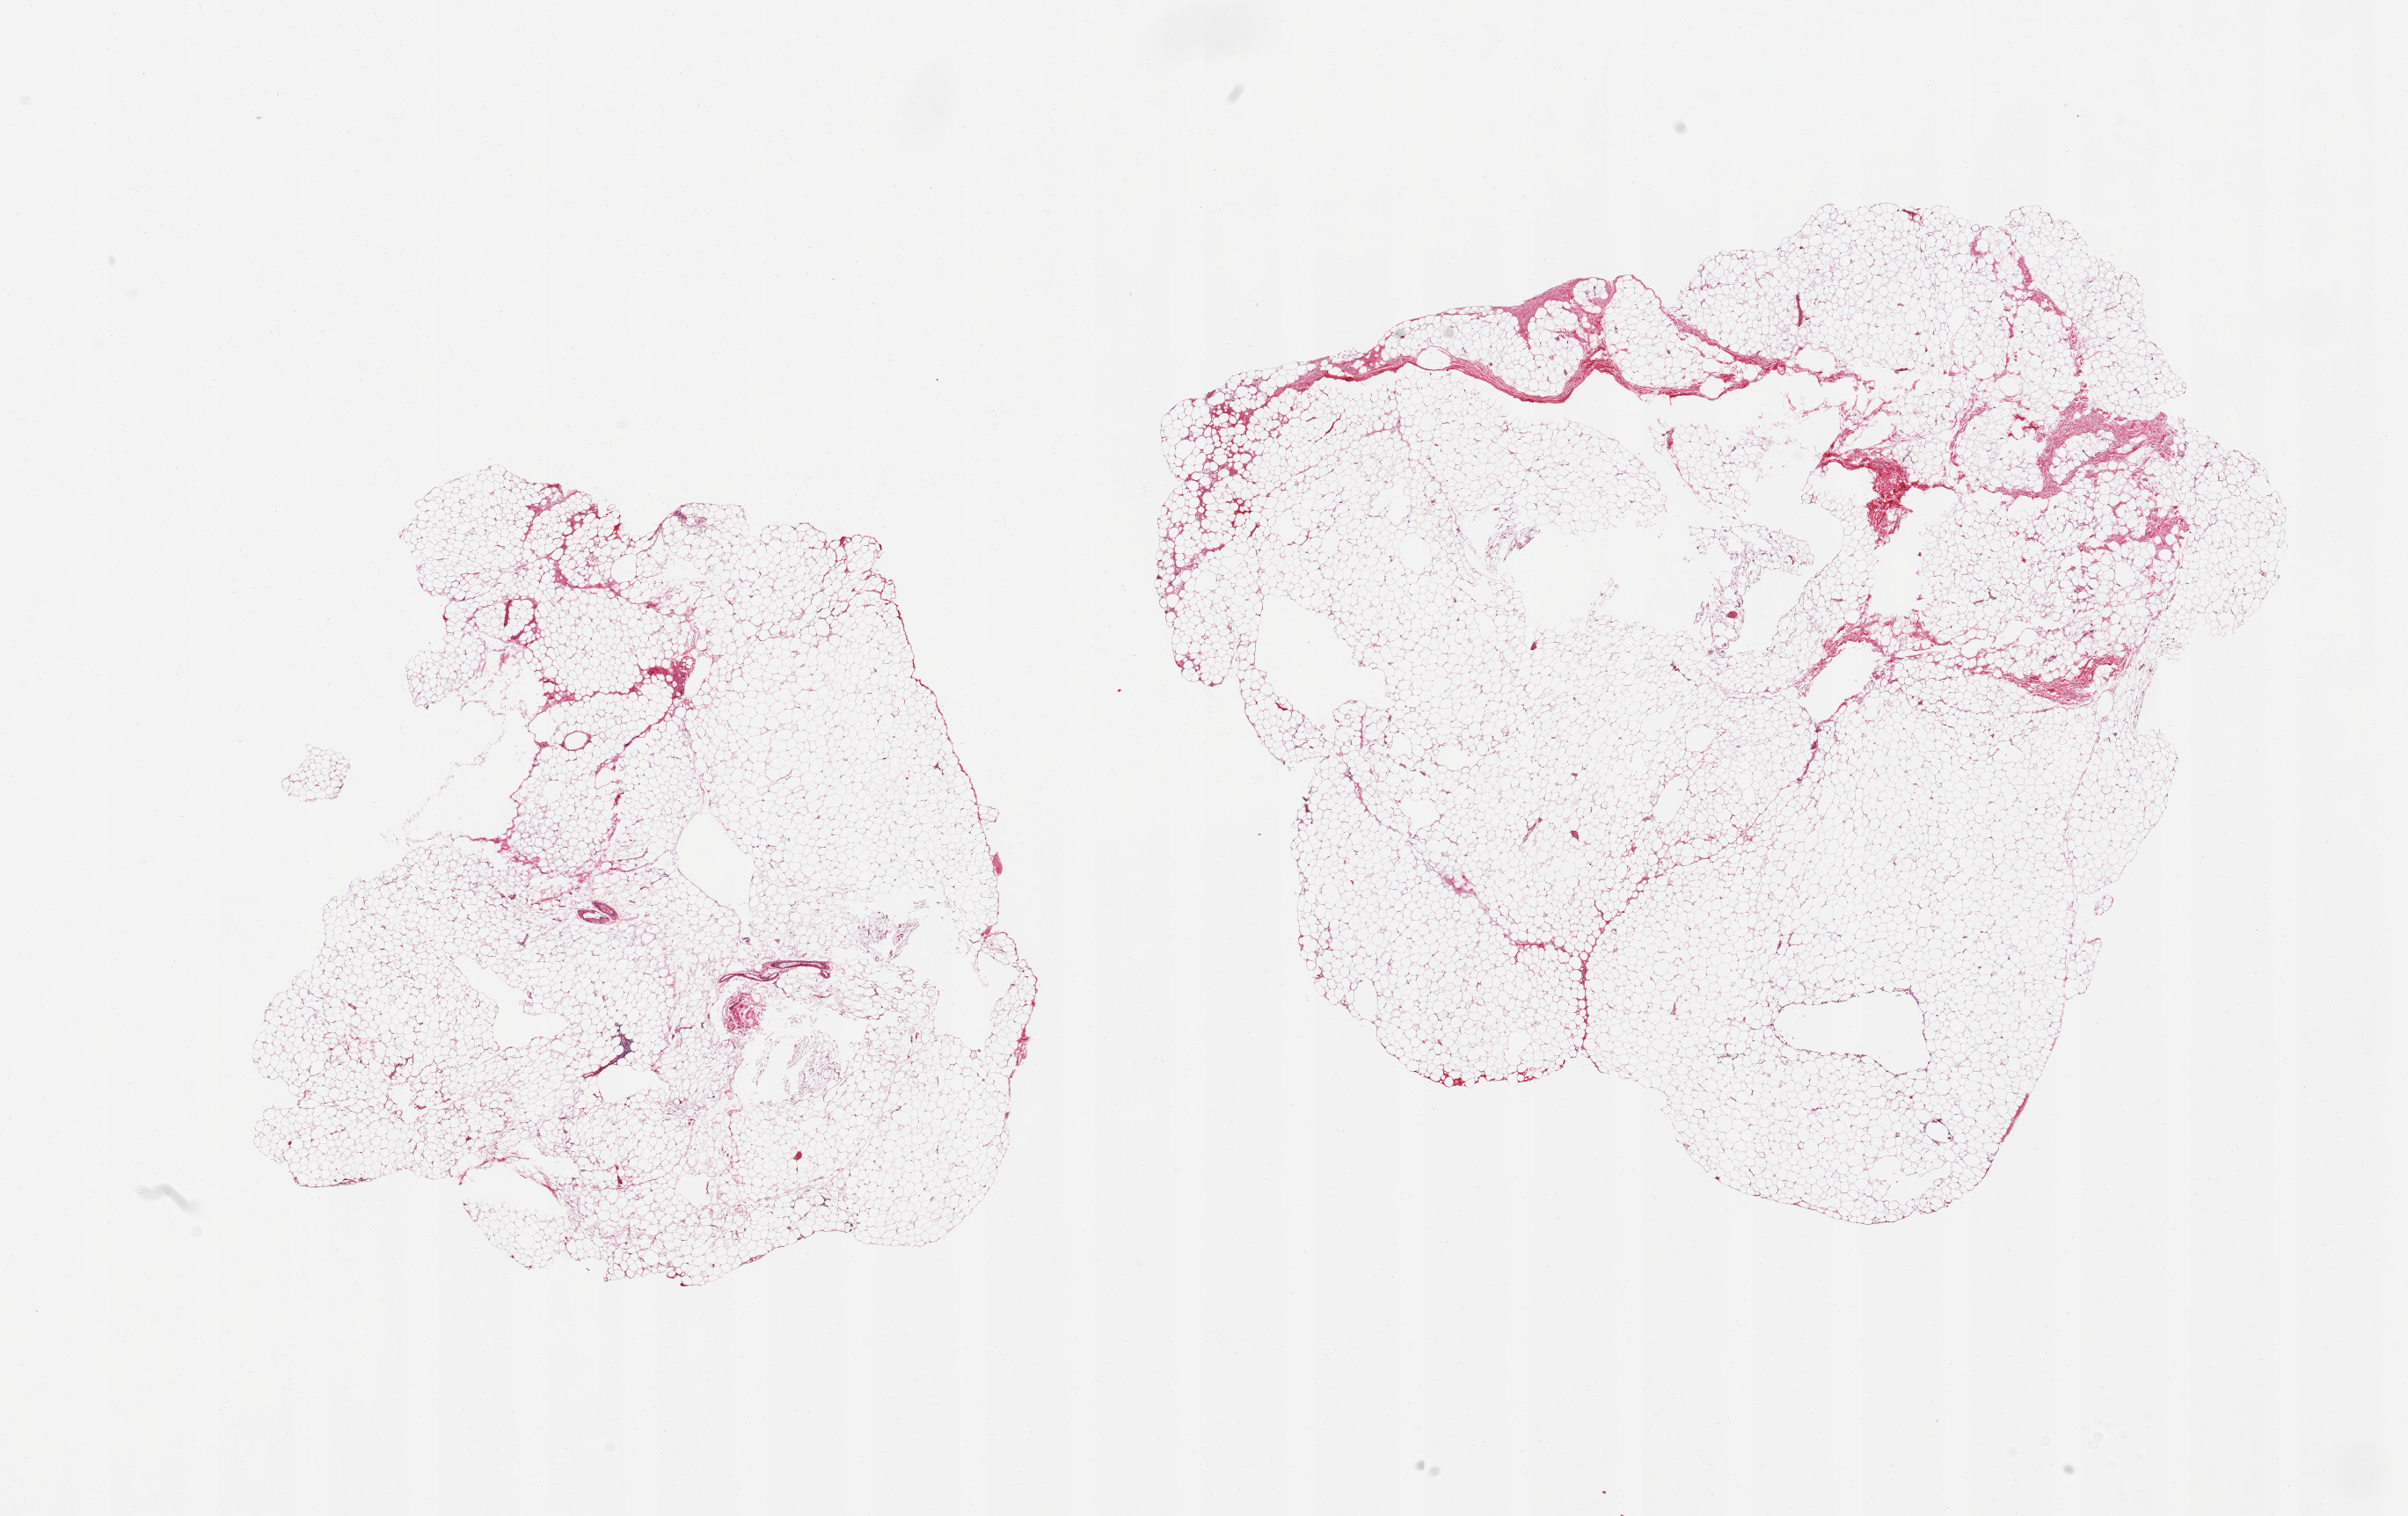
Digitized haematoxylin and eosin-stained section, a low-resolution overview of the entire scanned area, about 21.7 x 13.6 mm, PAXgene-fixed paraffin-embedded (PFPE) section, target tissue: breast, tissue donor sample. Donor sex: male.
Reviewer comment on this tissue sample: 2 pieces, fibroadipose elements only.